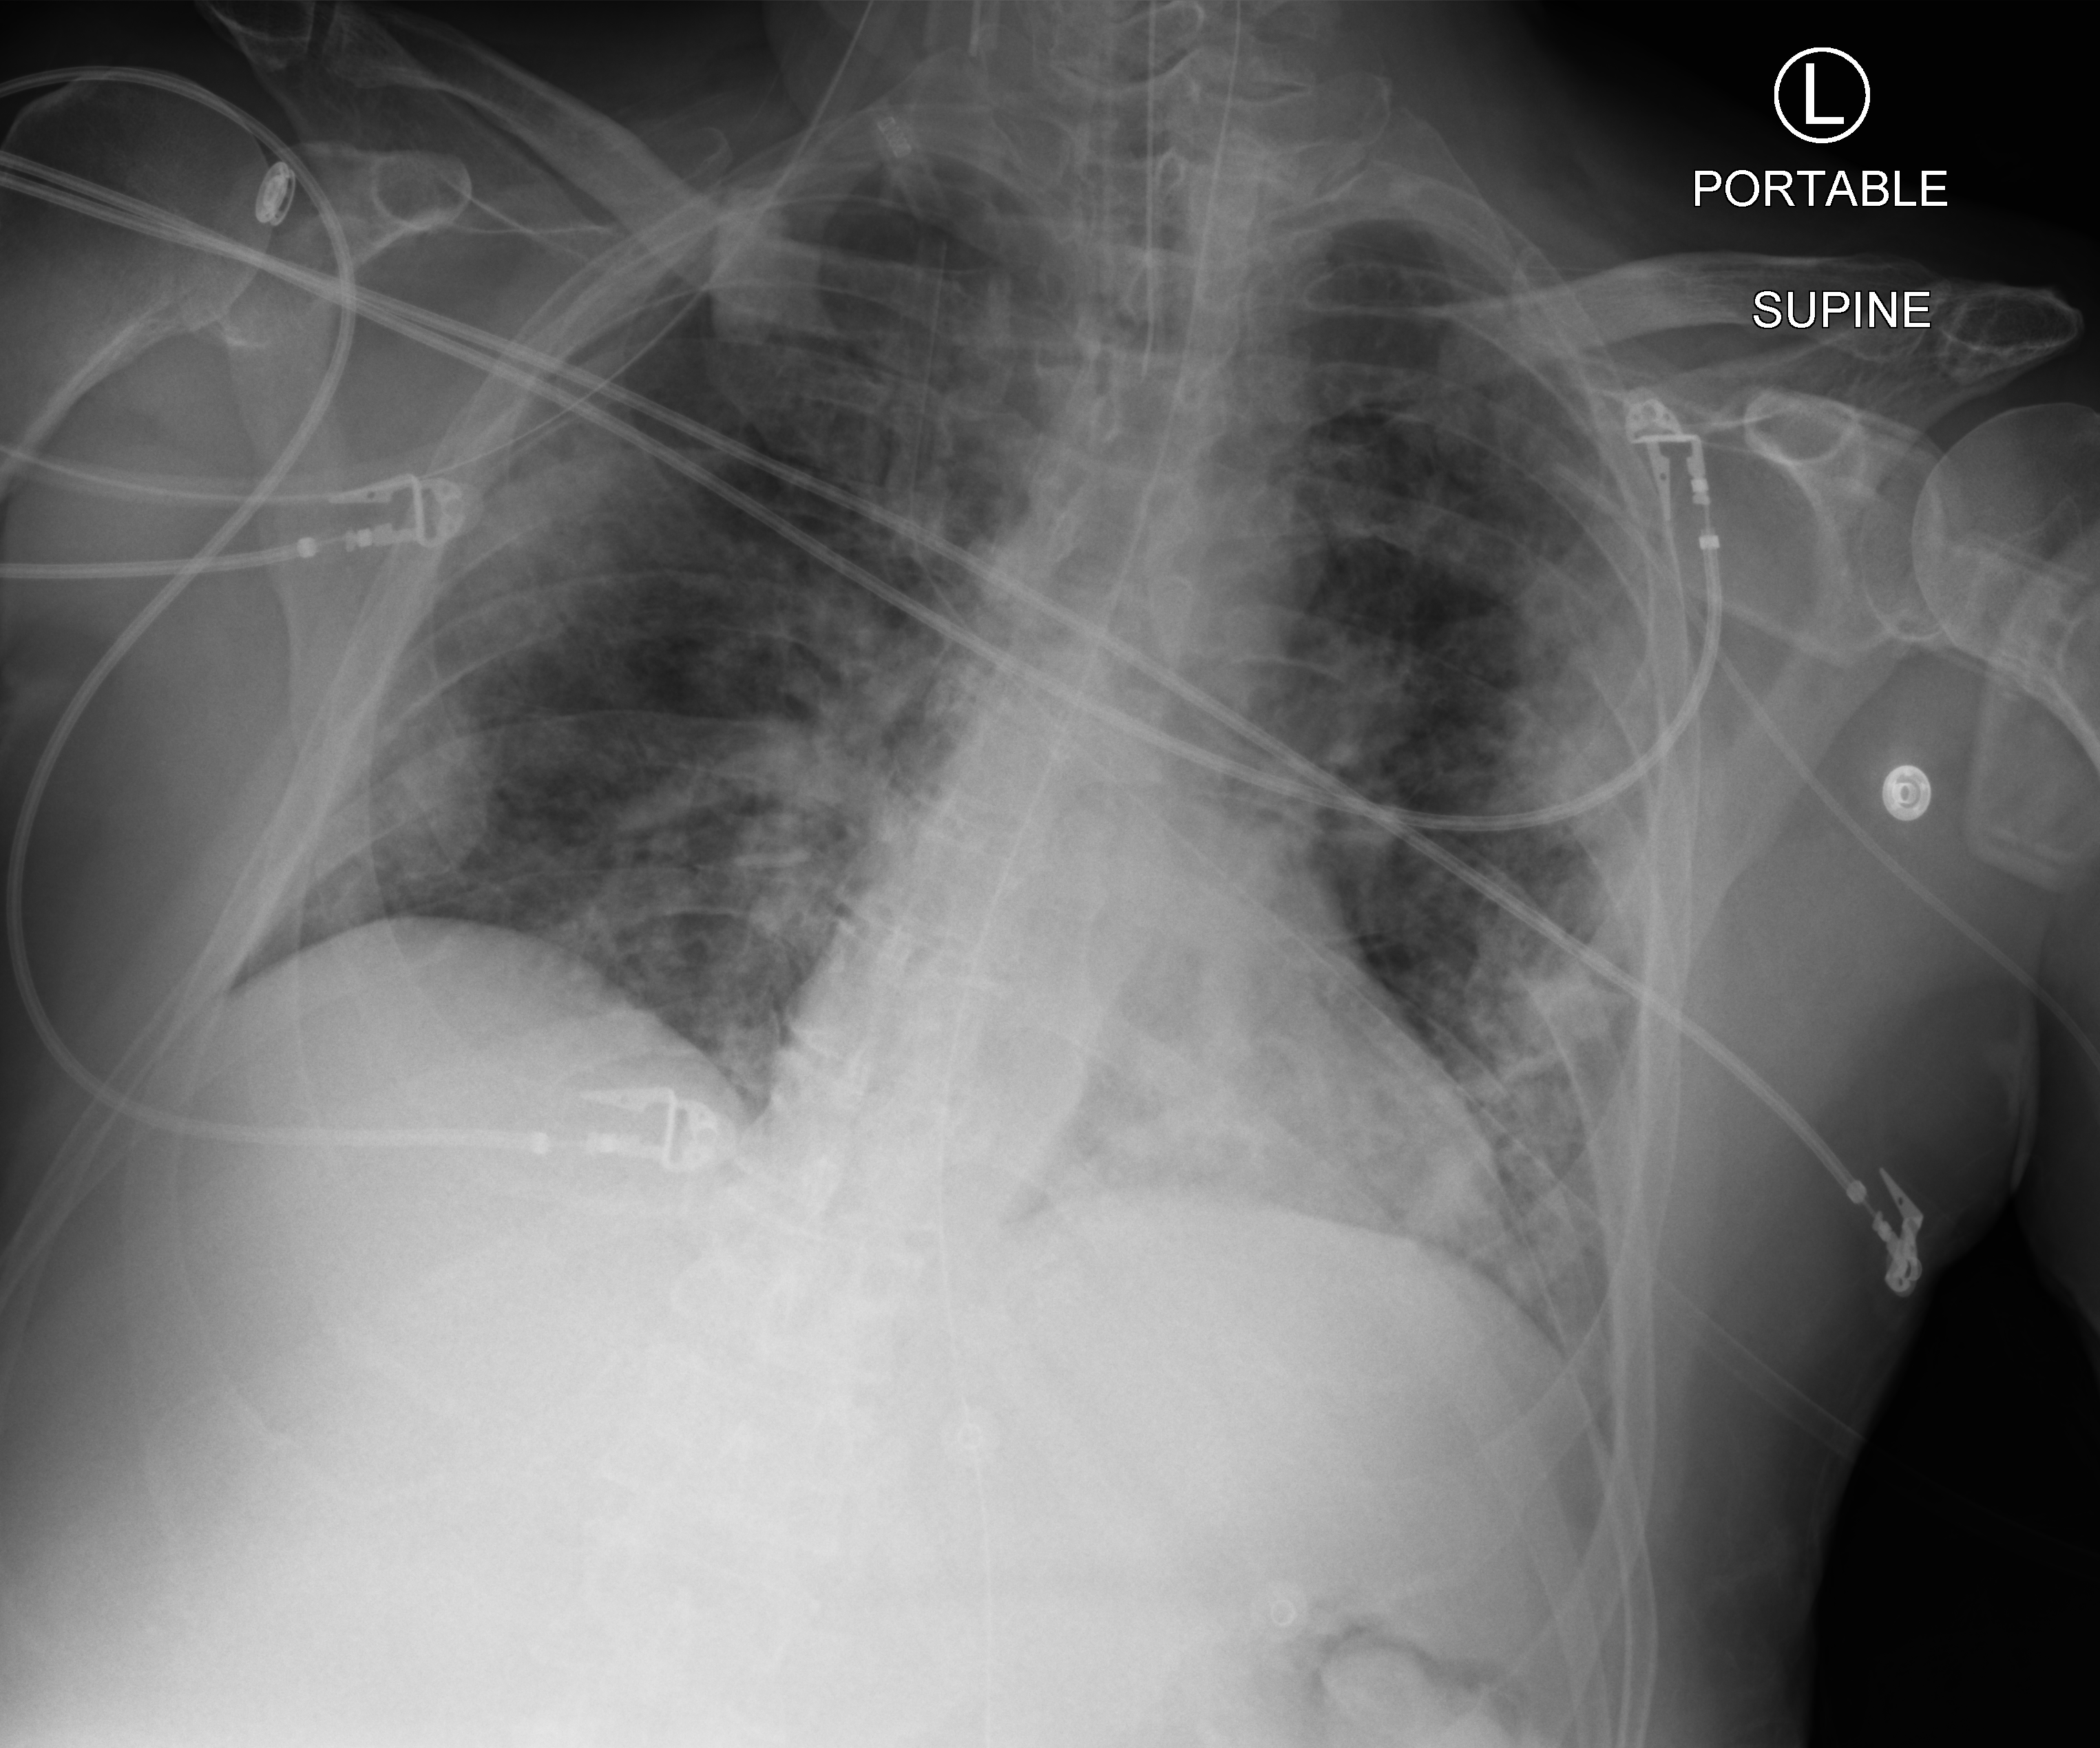
Bedside chest radiograph (computed radiography), anteroposterior (AP) projection. Male patient hospitalised with COVID-19, age 18–59 years.
Hospital-stay facts (about this admission, not read from this image; timing relative to this image not recorded): diabetes (admission record): no.